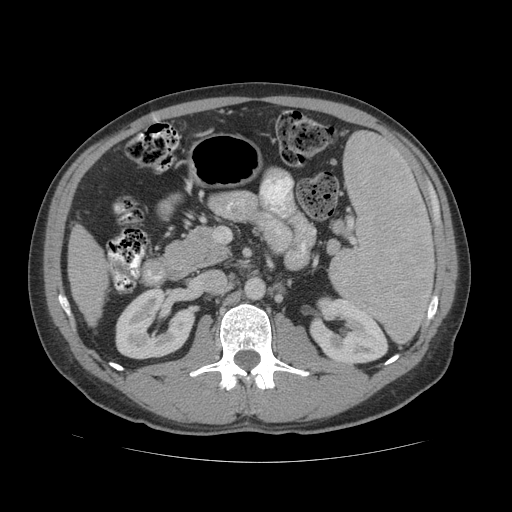
Contrast-enhanced abdominal CT (liver protocol), one axial slice; 140 kVp; soft-tissue window (W 400 / L 40 HU); 512 × 512 image matrix, field of view 400 × 400 mm. From the clinical record (not read from this slice): diagnosis: hepatocellular carcinoma (patient treated with transarterial chemoembolisation; whether this scan precedes or follows treatment is not stated here); TNM stage (as recorded): Stage-IVB; Child-Pugh class: B; tumour differentiation: well differentiated; tumour nodularity: multinodular.
Structures marked on this image (semi-automatically segmented with operator editing):
- liver parenchyma outside the tumour (the mass and vessels are separate outlines, so this box may not span the whole liver): box from (x=68, y=226) to (x=108, y=324) px